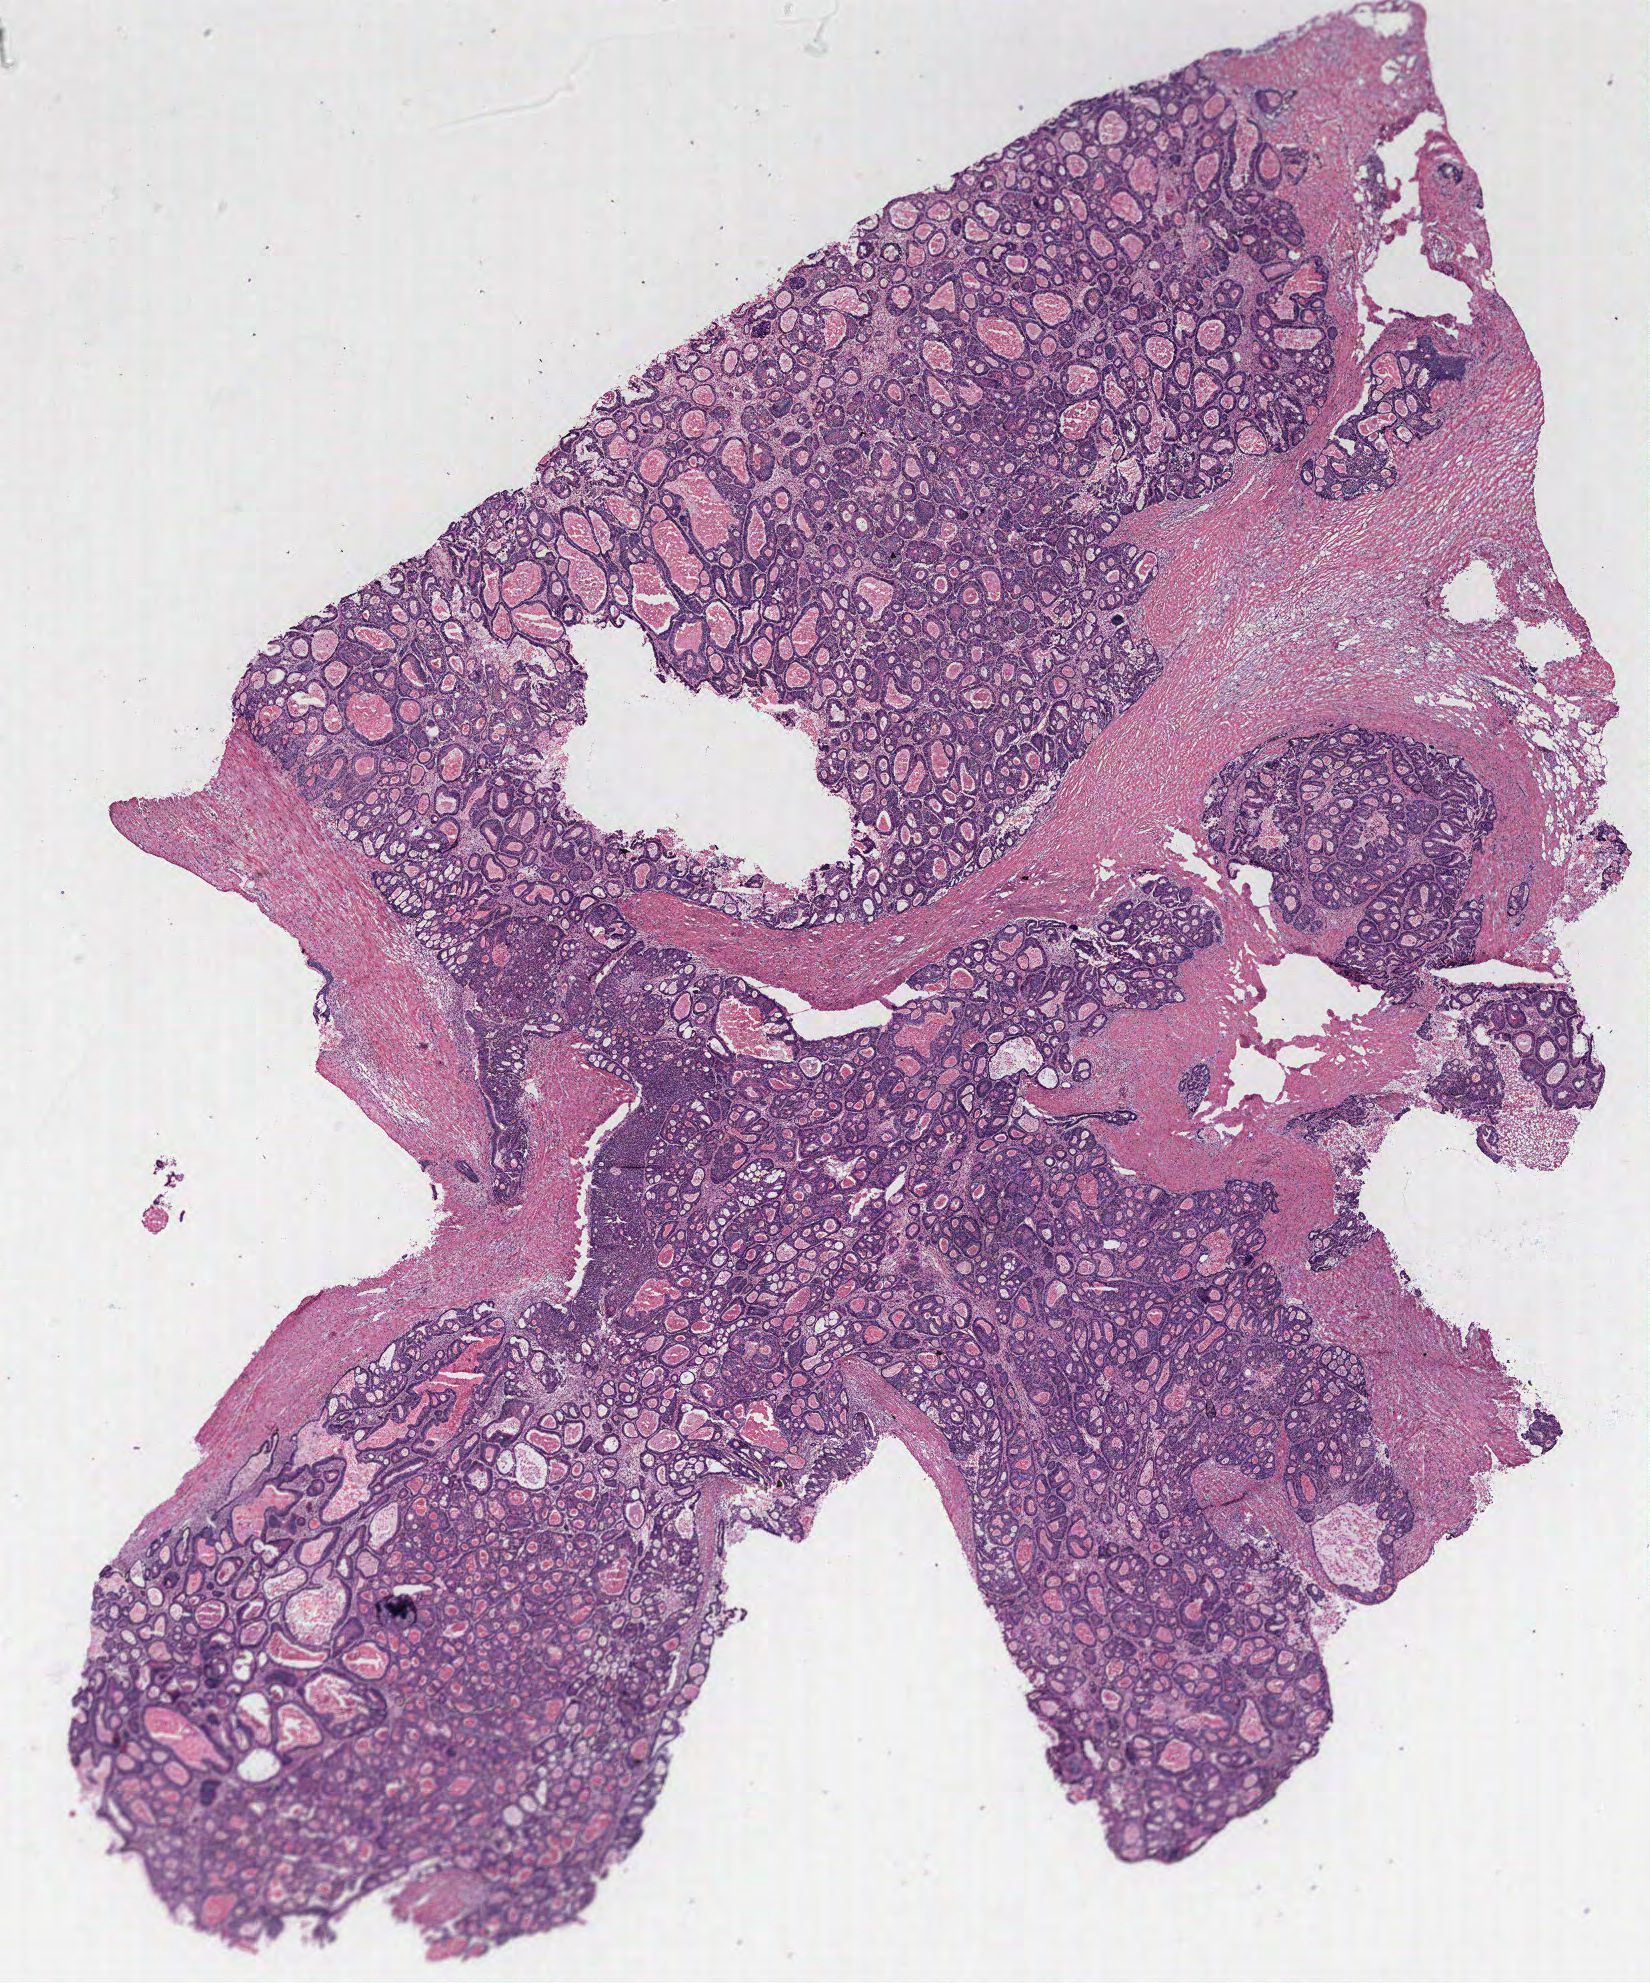
Digitized H&E-stained tissue section (whole slide), a low-resolution overview of the entire scanned area, about 13.2 x 15.9 mm (from a 40x scan), colon, tissue type not recorded. Male patient.
Patient diagnosis: Adenocarcinoma, NOS.